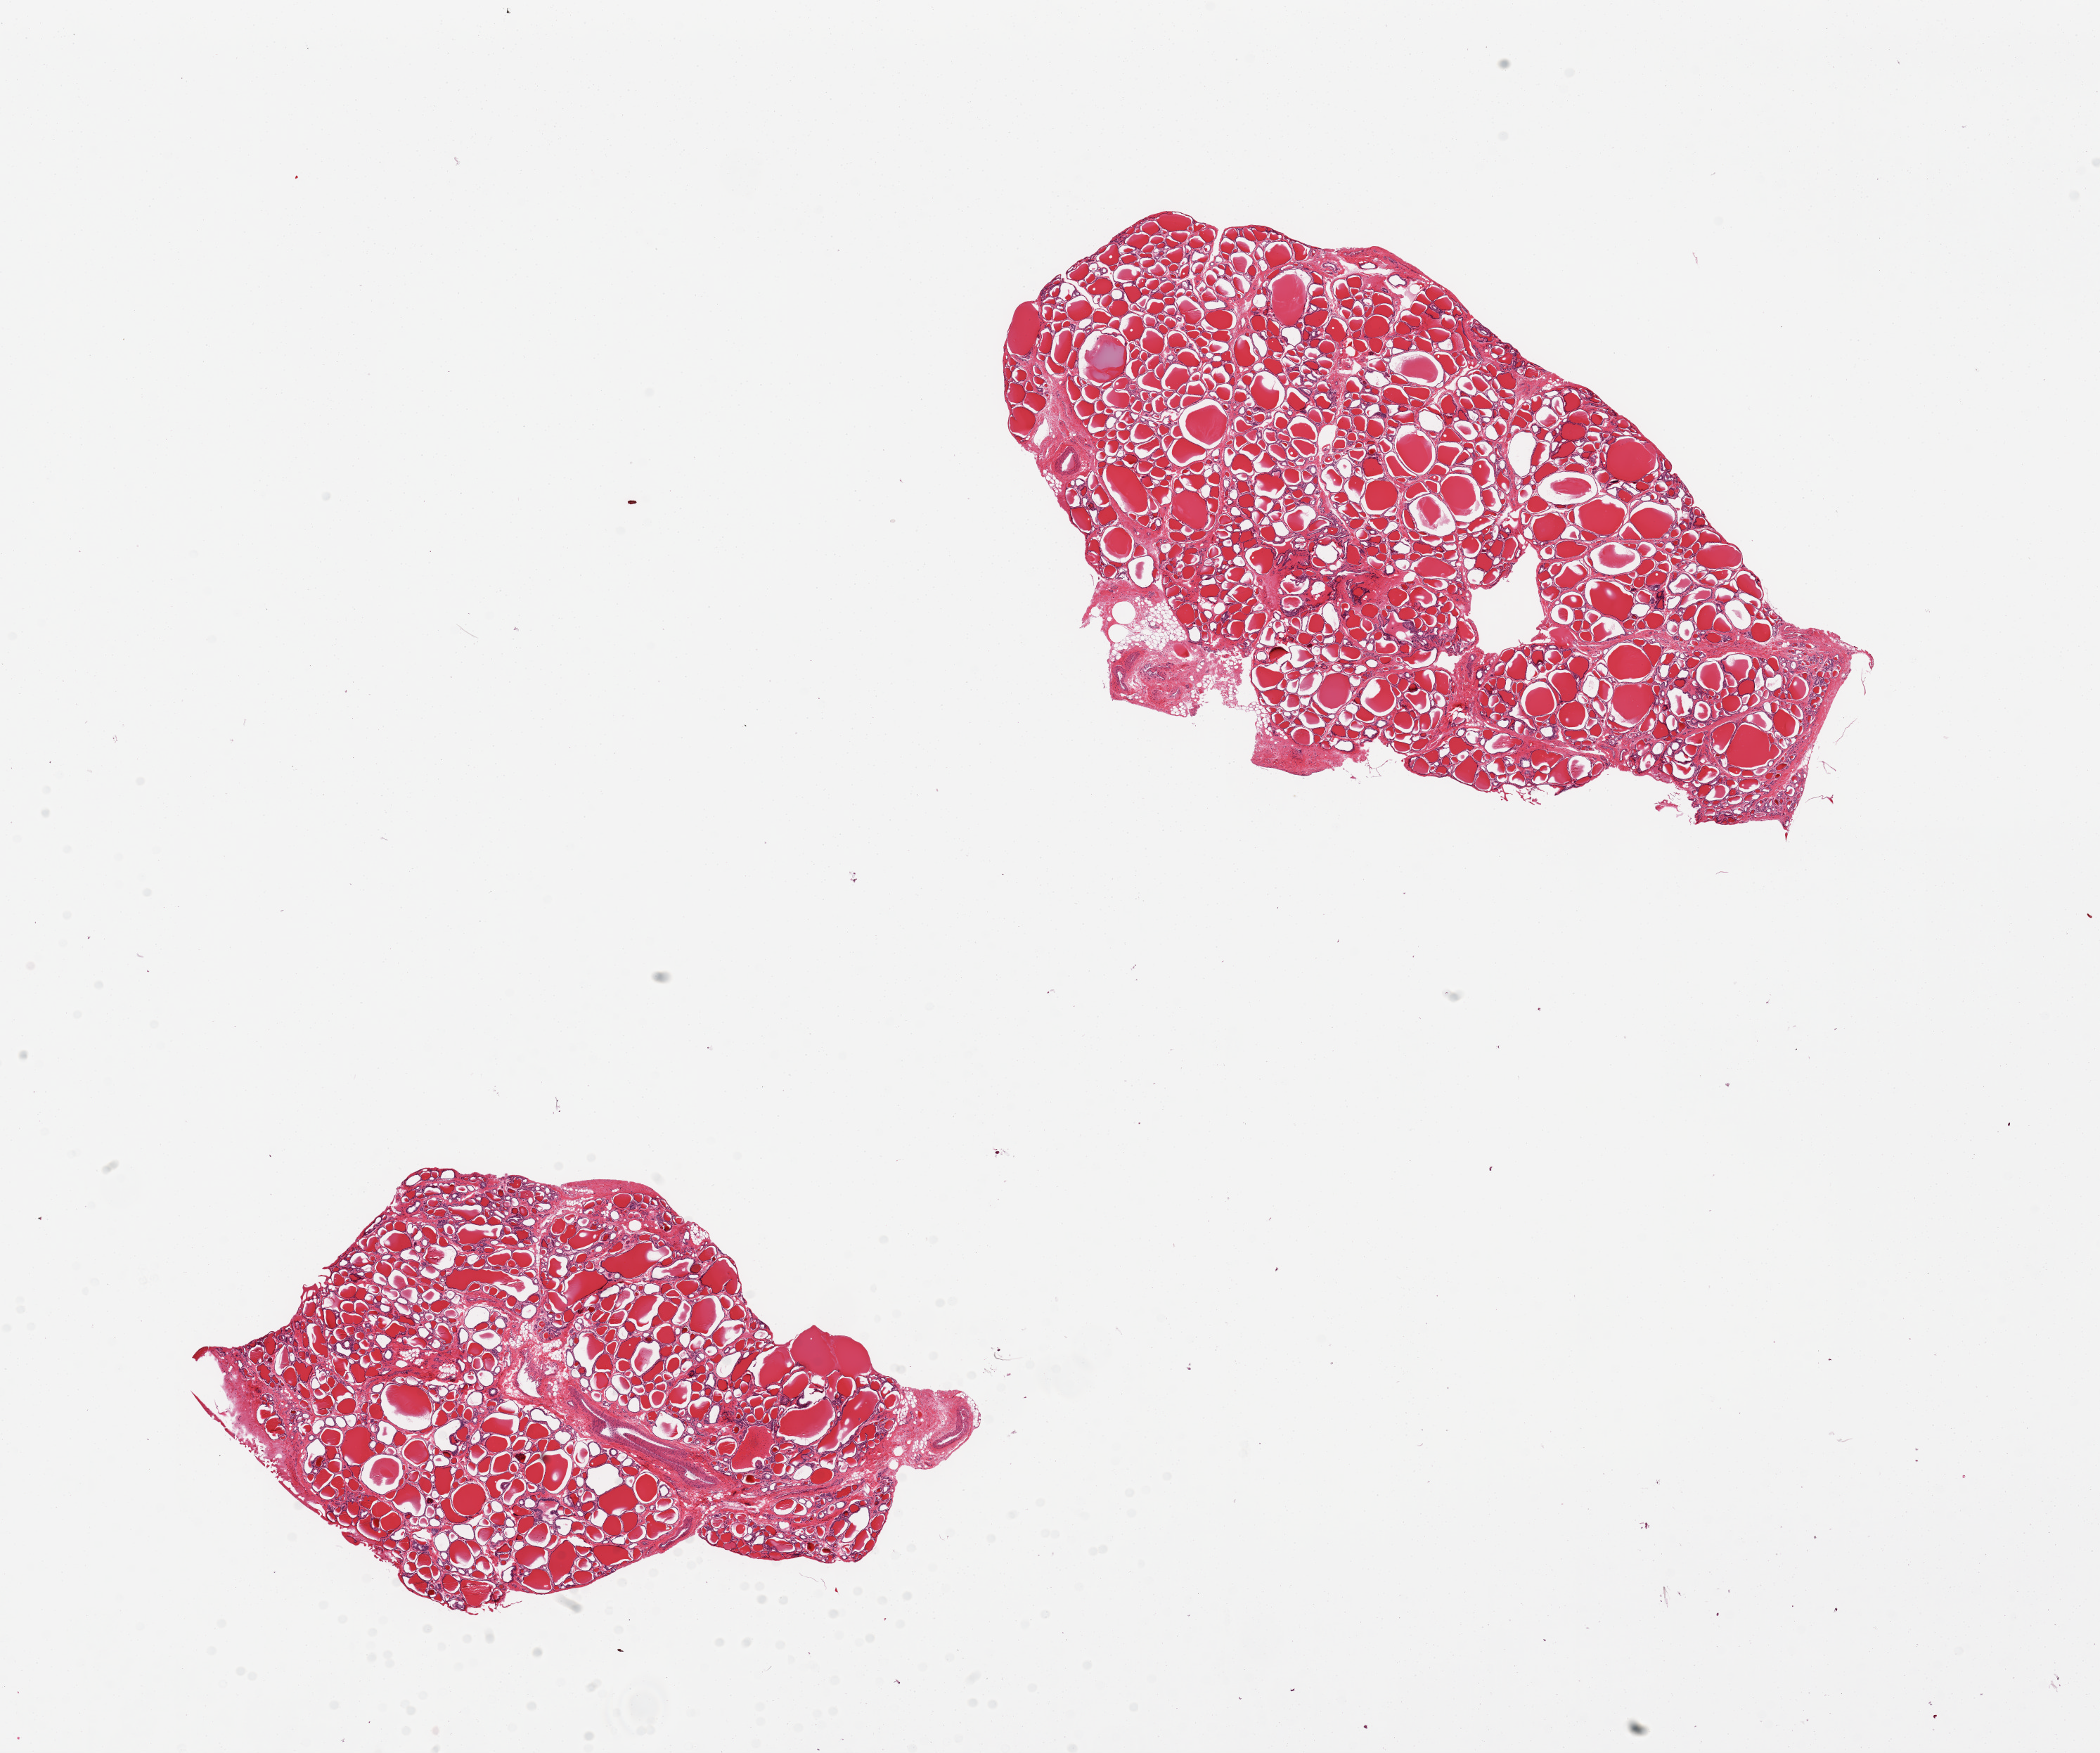
Whole-slide image, hematoxylin and eosin (H&E) stain, shown as a low-resolution overview of the whole scanned area (about 23.6 x 19.7 mm, slide scanned at 20x). PAXgene-fixed paraffin-embedded (PFPE) section. Sampled site (target tissue): thyroid. Tissue donor sample. Donor sex: male.
Pathologist's review note for this sample: 2 pieces.